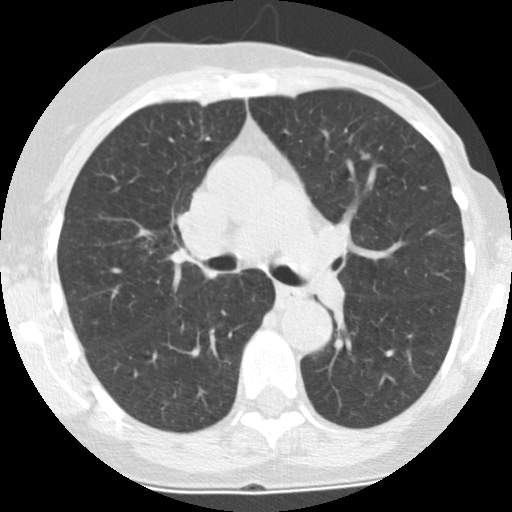
Chest CT (low-dose screening protocol), one axial image, baseline annual screen, lung window (W 1500 / L -600 HU), 2.5 mm slice thickness, slice 94 of 225 in the series, 512 × 512 image matrix, field of view 280 × 280 mm. Female participant, aged 66 years at enrolment.
Expert reader's lesion annotation, bounding box [x1, y1, x2, y2] px = [358, 146, 373, 166]. Screening reader's record for this exam: no non-calcified nodule ≥4 mm recorded. Official screen result: negative screen, minor abnormalities not suspicious for lung cancer. Participant outcome: lung cancer diagnosed 583 days after this screen (after the second annual screen) — adenocarcinoma, NOS, left lower lobe, poorly differentiated (G3), stage IA (AJCC 6th edition), 8 mm at pathology.